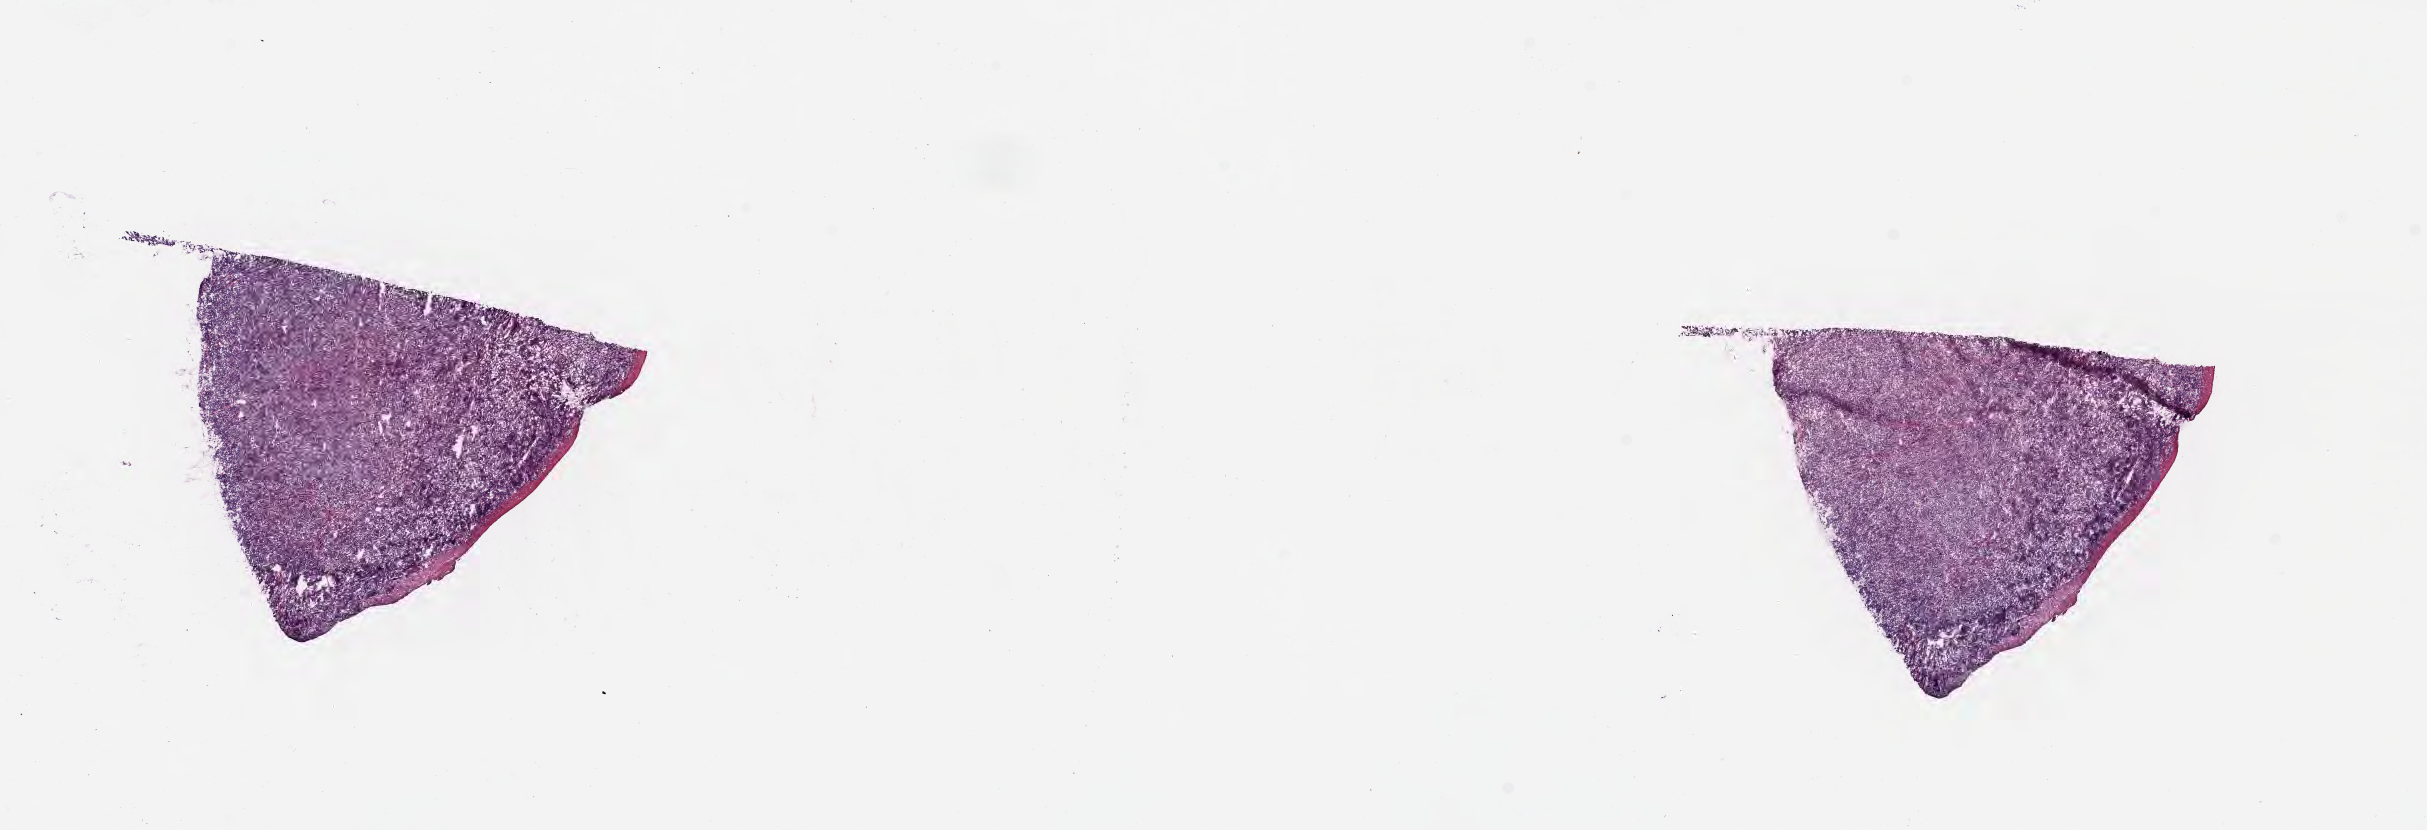
Haematoxylin and eosin whole-slide image, low-resolution overview of the scanned area, about 19.6 x 6.7 mm. Frozen section (tissue freezing medium). Primary tumor. Anatomic site: cranium. Patient: male, age 13 years. Composition of this section per pathologist review: tumor cells 85%, tumor nuclei 90%, stromal cells 10%, necrosis 5%, normal cells 0%. Inflammatory infiltration, as recorded: lymphocyte infiltration 30%, monocyte infiltration 40%, neutrophil infiltration 5%.
• diagnosis: Diffuse large B-cell lymphoma, NOS
• Ann Arbor stage (patient): Stage III